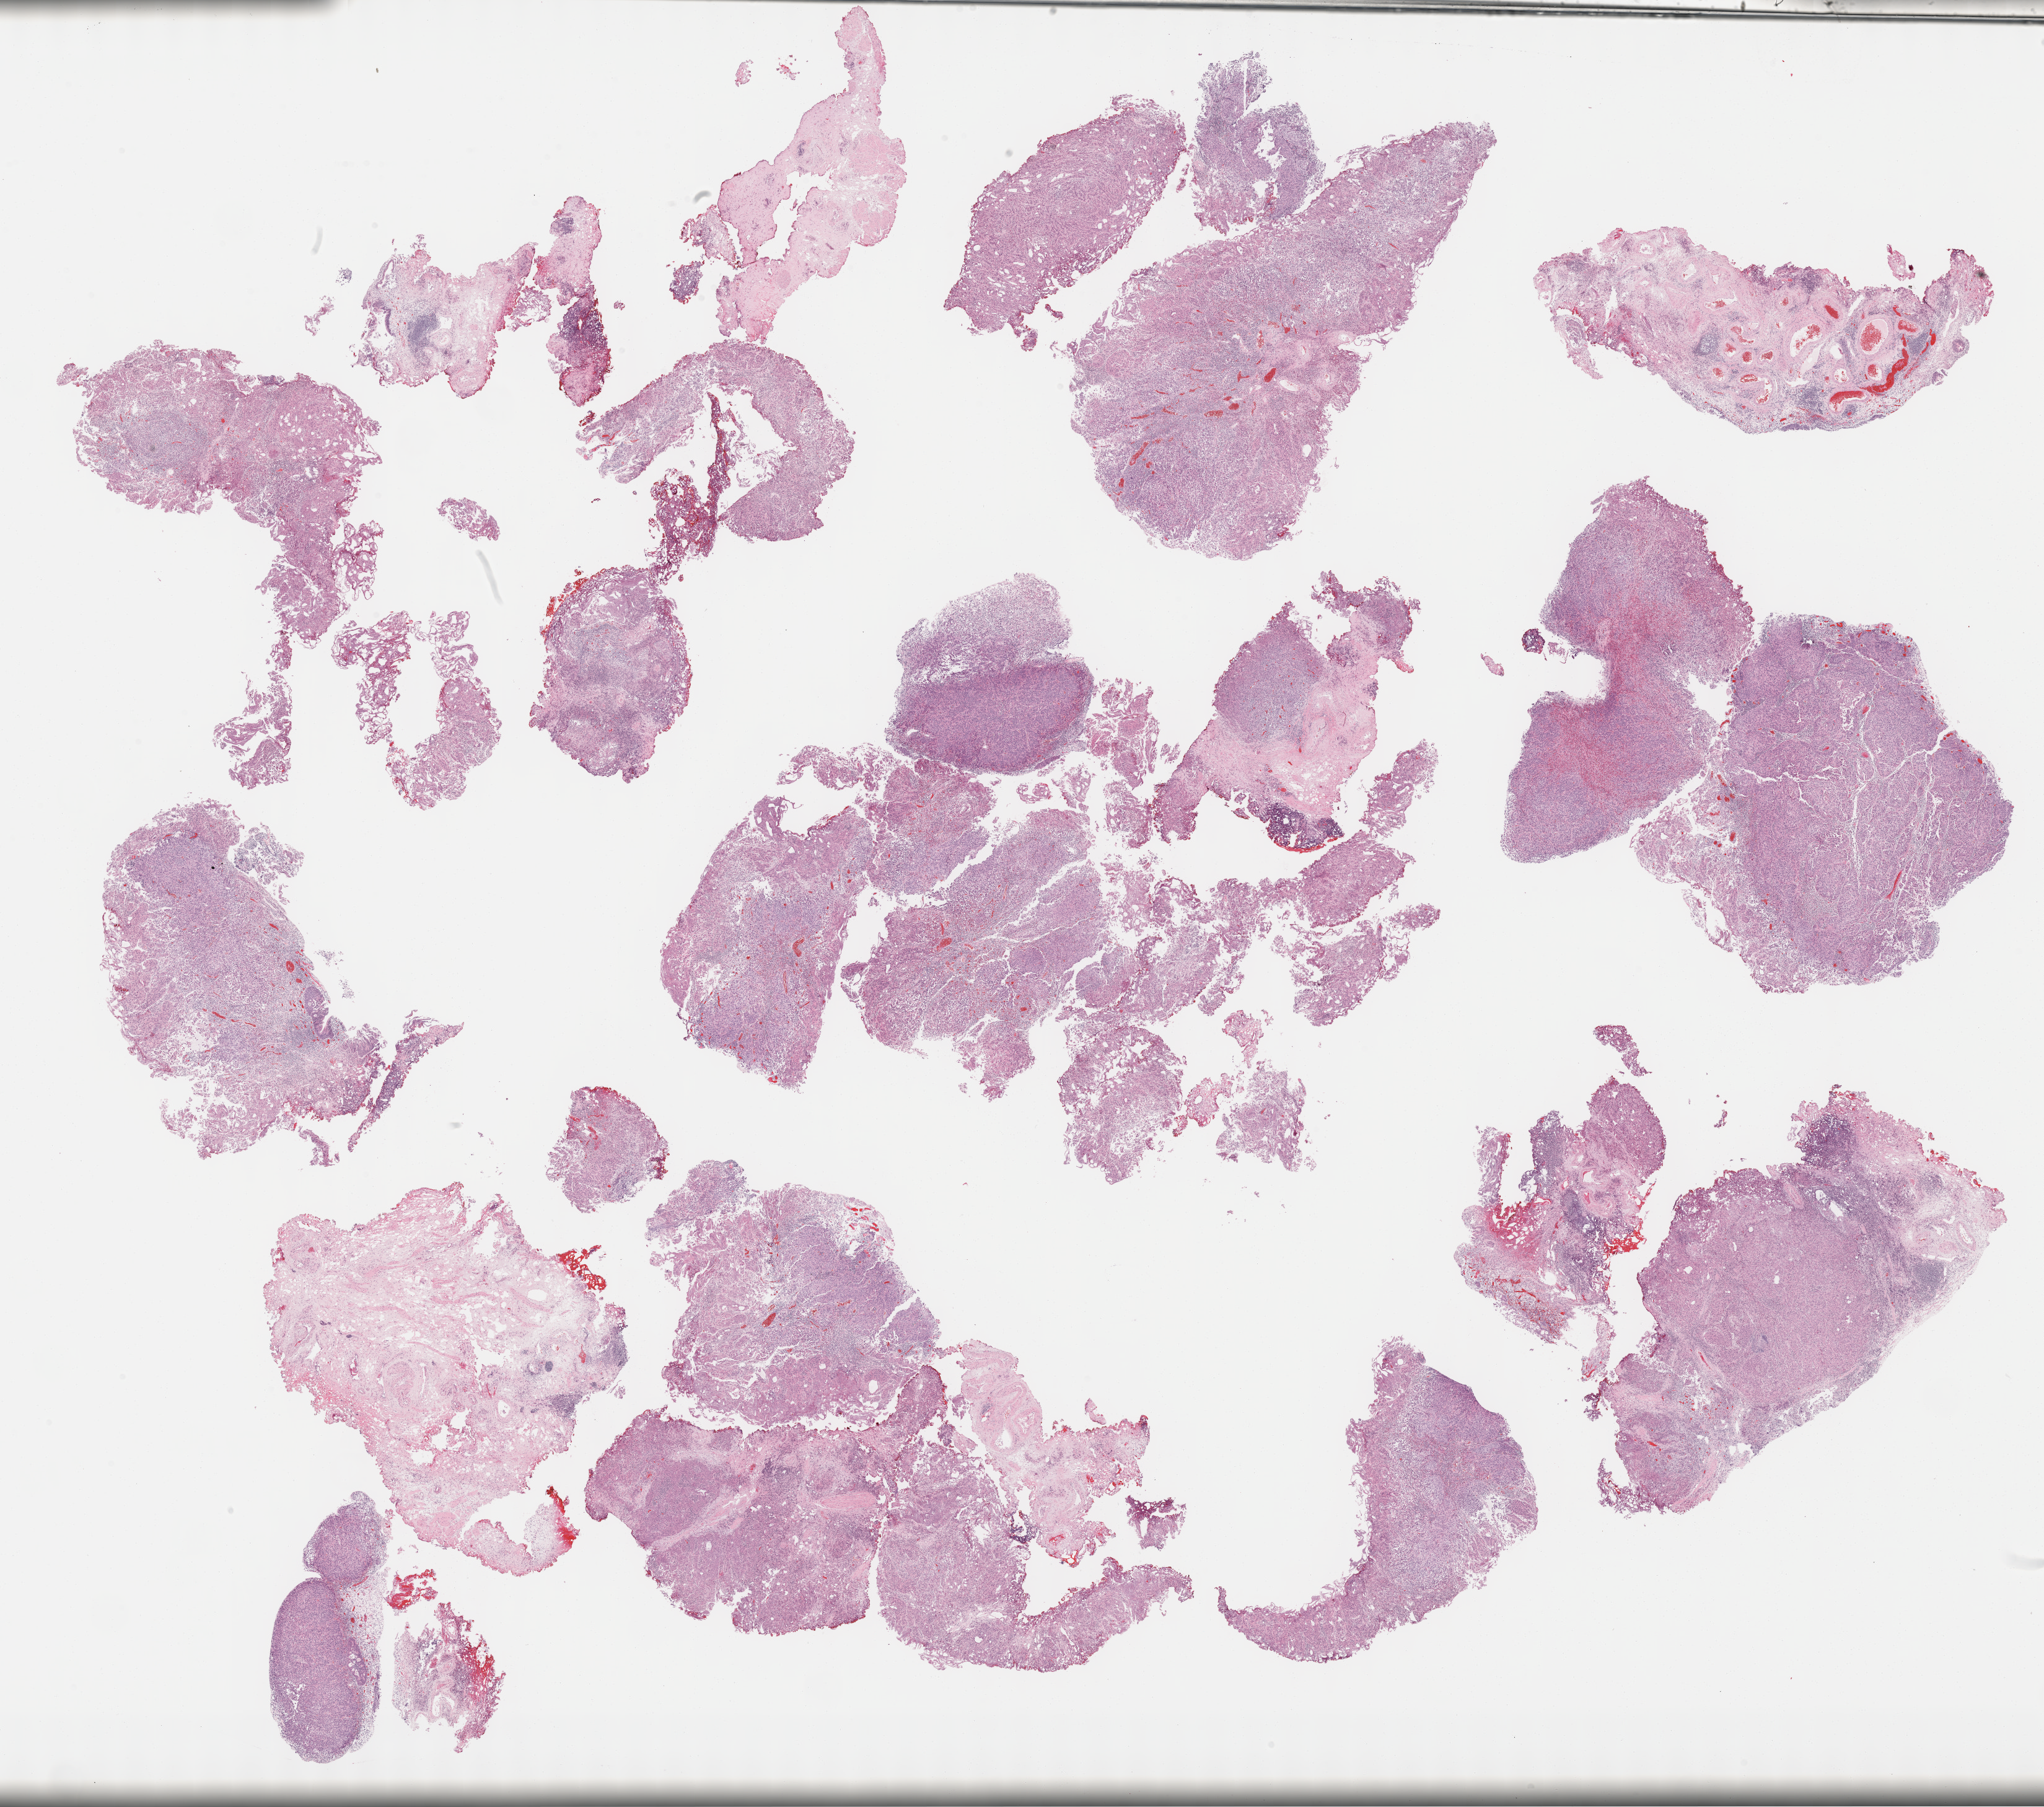
Digitized H&E-stained tissue section (whole slide) — low-resolution overview of the scanned area, about 26.7 x 23.6 mm (acquisition: 40x scan). FFPE section. Primary tumour sample from the bladder. Patient: male, age at initial diagnosis 57 years. Histologic grade: high grade.
TNM: NX MX. Histologic diagnosis: Transitional cell carcinoma (posterior wall of bladder). AJCC pathologic stage: II.